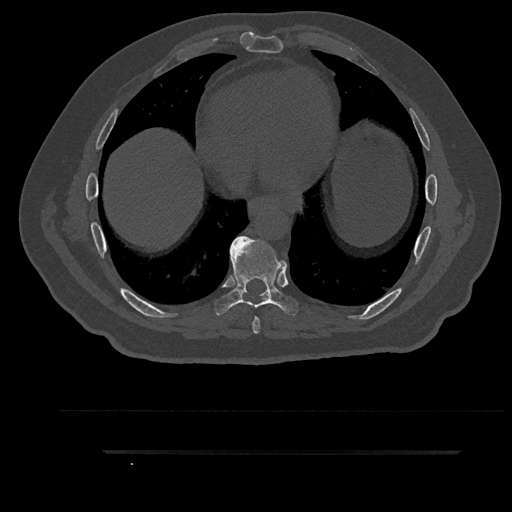
CT including the spine, one axial slice. Position 486 of 797 along the scan axis. Reconstruction kernel Br40s/3. 120 kVp. Bone window (W 1800 / L 400 HU). 0.5 mm slice thickness. 512 × 512 image matrix, field of view 432 × 432 mm. Patient: male, 63 years. Case-level facts recorded for this patient, not image findings: primary cancer: renal; vertebrae with lytic lesions (as recorded): T8.
Annotated regions visible in this slice (semi-automatically segmented with operator editing):
- T7 vertebra: box from (x=243, y=239) to (x=260, y=334) px
- T8 vertebra: (x=214, y=236)–(x=298, y=316)